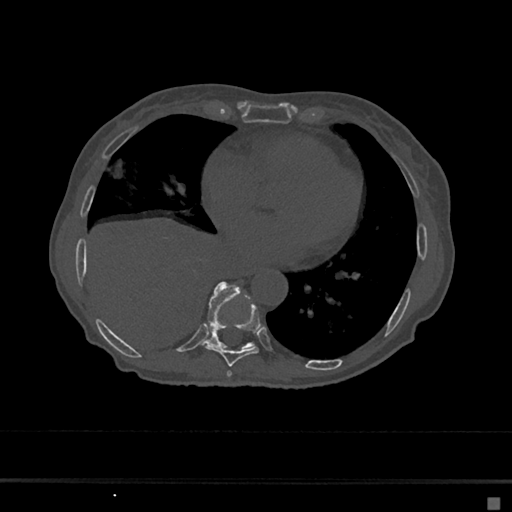
CT including the spine, one axial slice; position 305 of 797 along the scan axis; bone window (W 1800 / L 400 HU); 512 × 512 image matrix. Female patient, age 68 years. From the clinical record (not read from this slice): primary cancer: renal.
Annotated regions visible in this slice (semi-automatic segmentation, software-assisted and operator-edited):
- T7 vertebra: bounding box (x1, y1, x2, y2) in pixels: (227, 371, 232, 378)
- T8 vertebra: (205, 303, 260, 367)
- T9 vertebra: (207, 282, 254, 349)